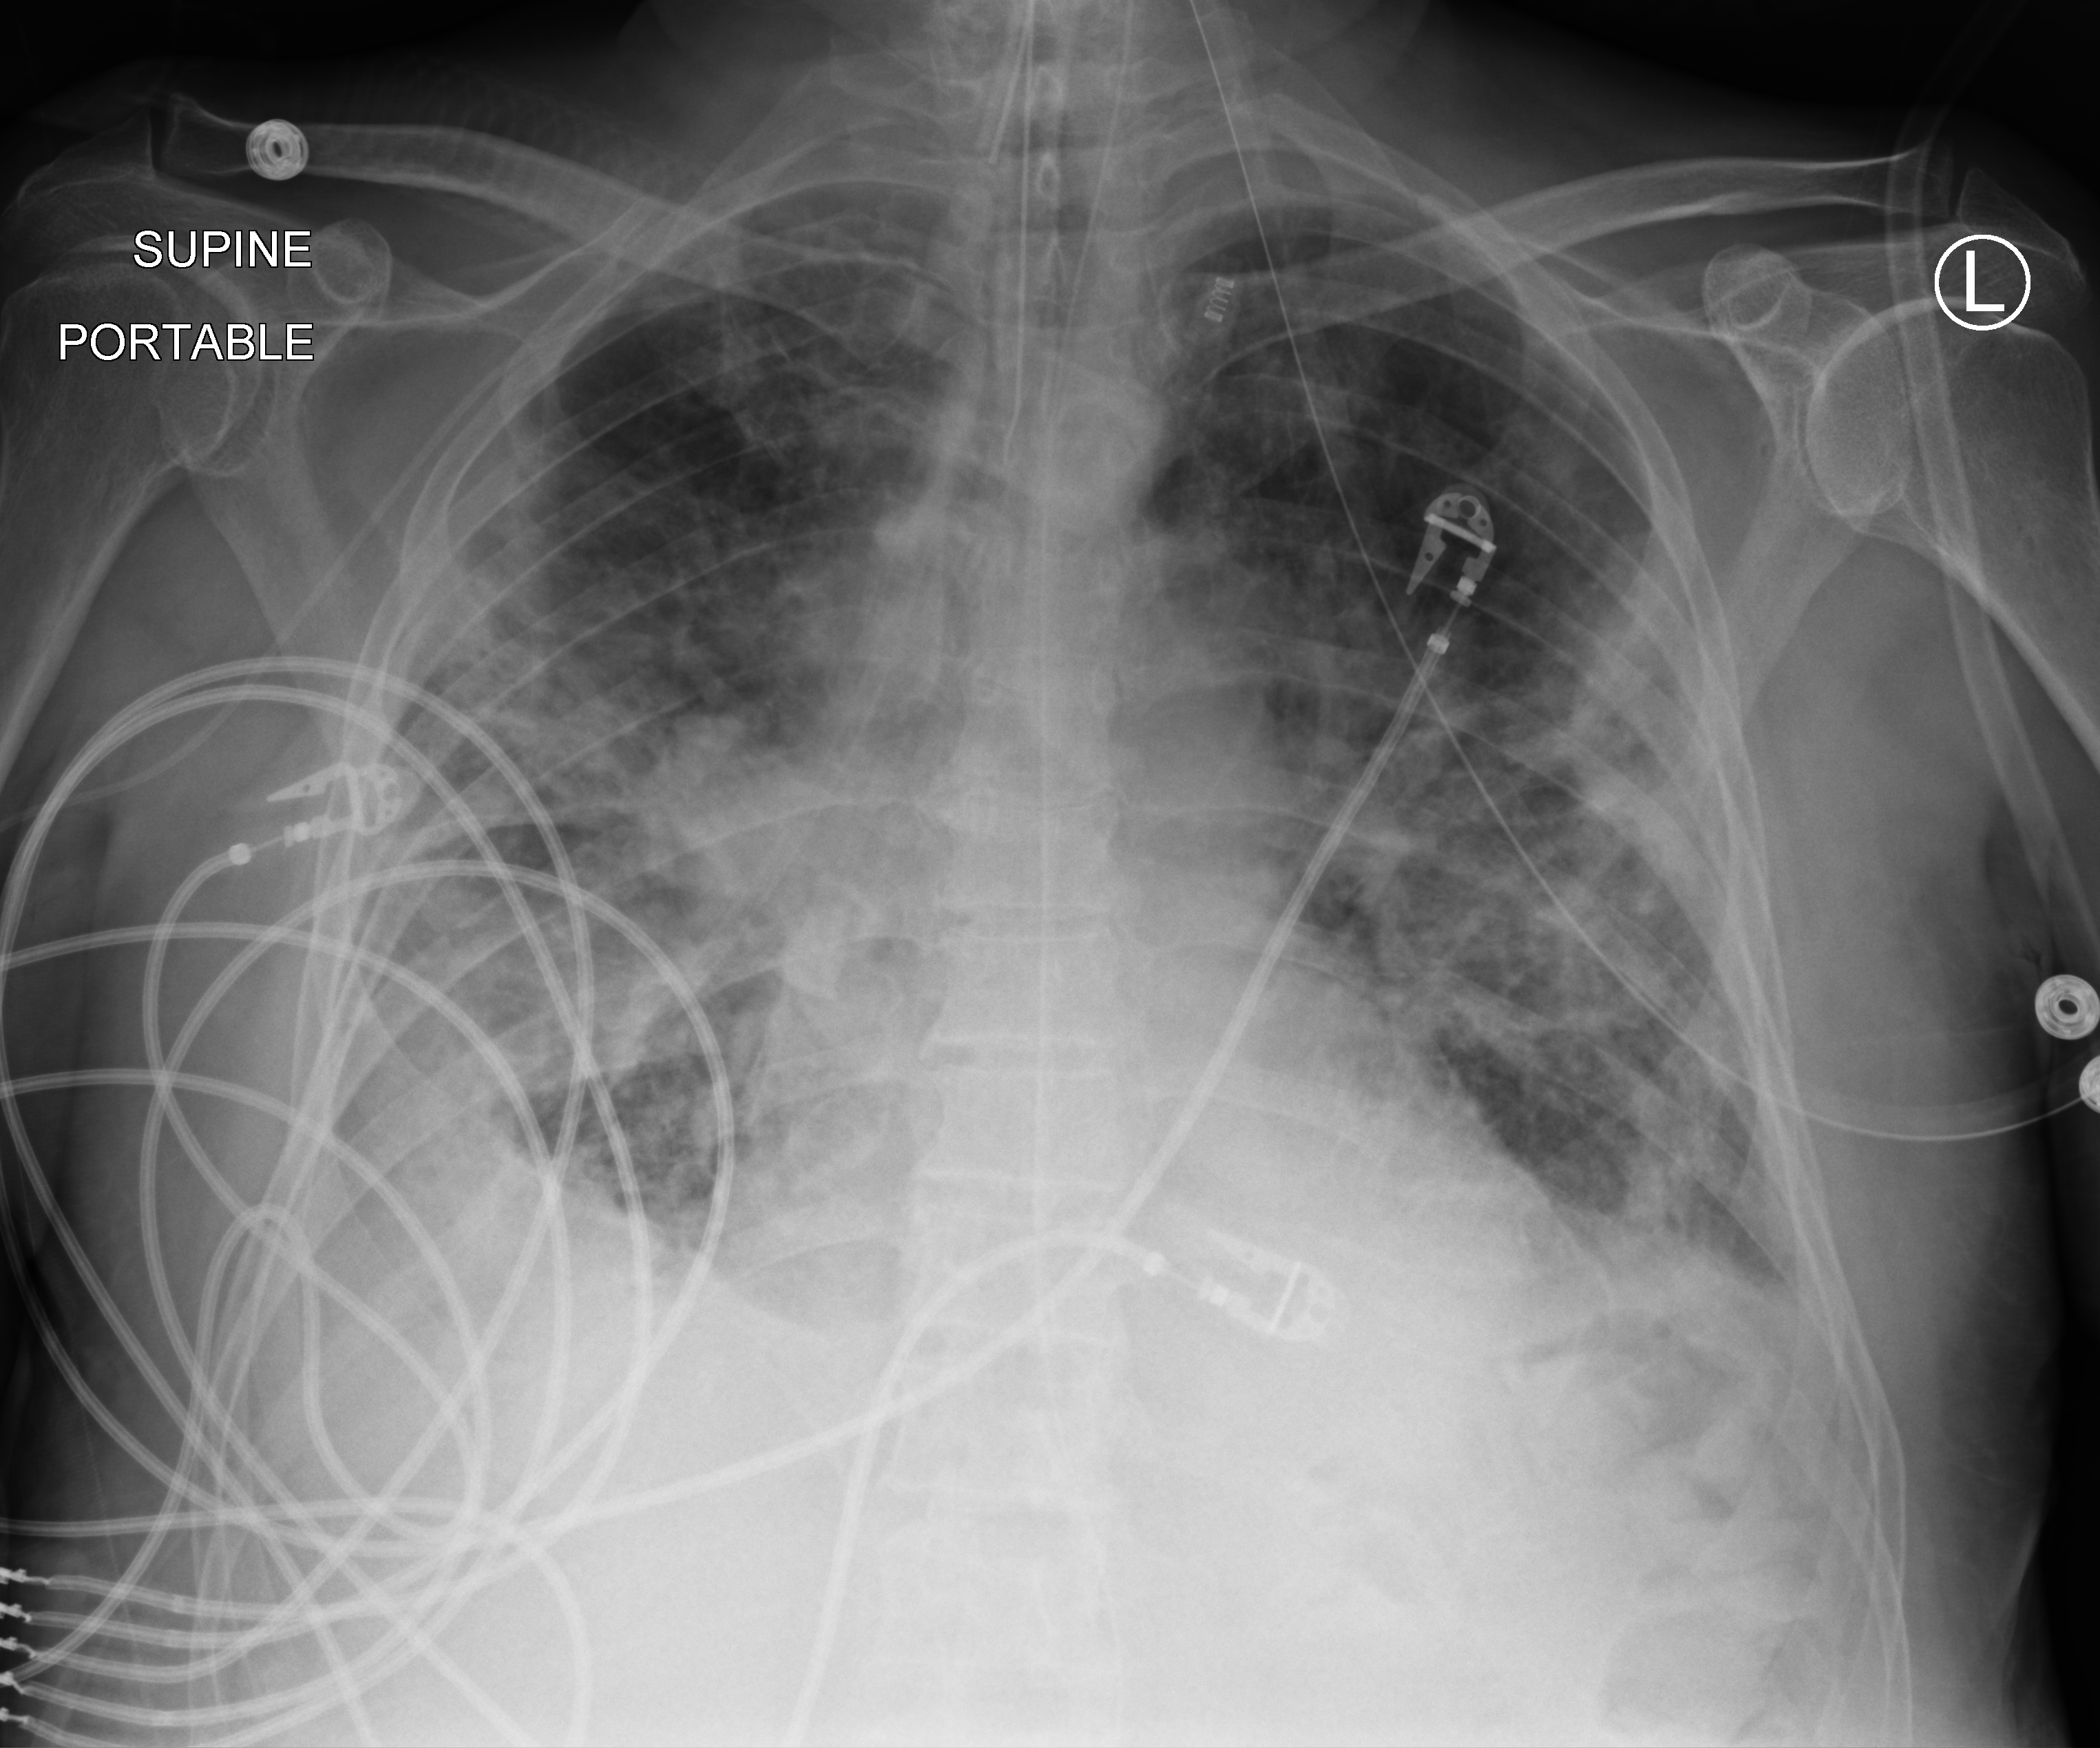
Portable chest radiograph, anteroposterior (AP) projection. Male patient hospitalised with COVID-19, age 75–90 years.
Admission-level facts for this patient (not findings on this image; timing relative to this image not recorded): diabetes (admission record): no; smoking status (admission record): never.